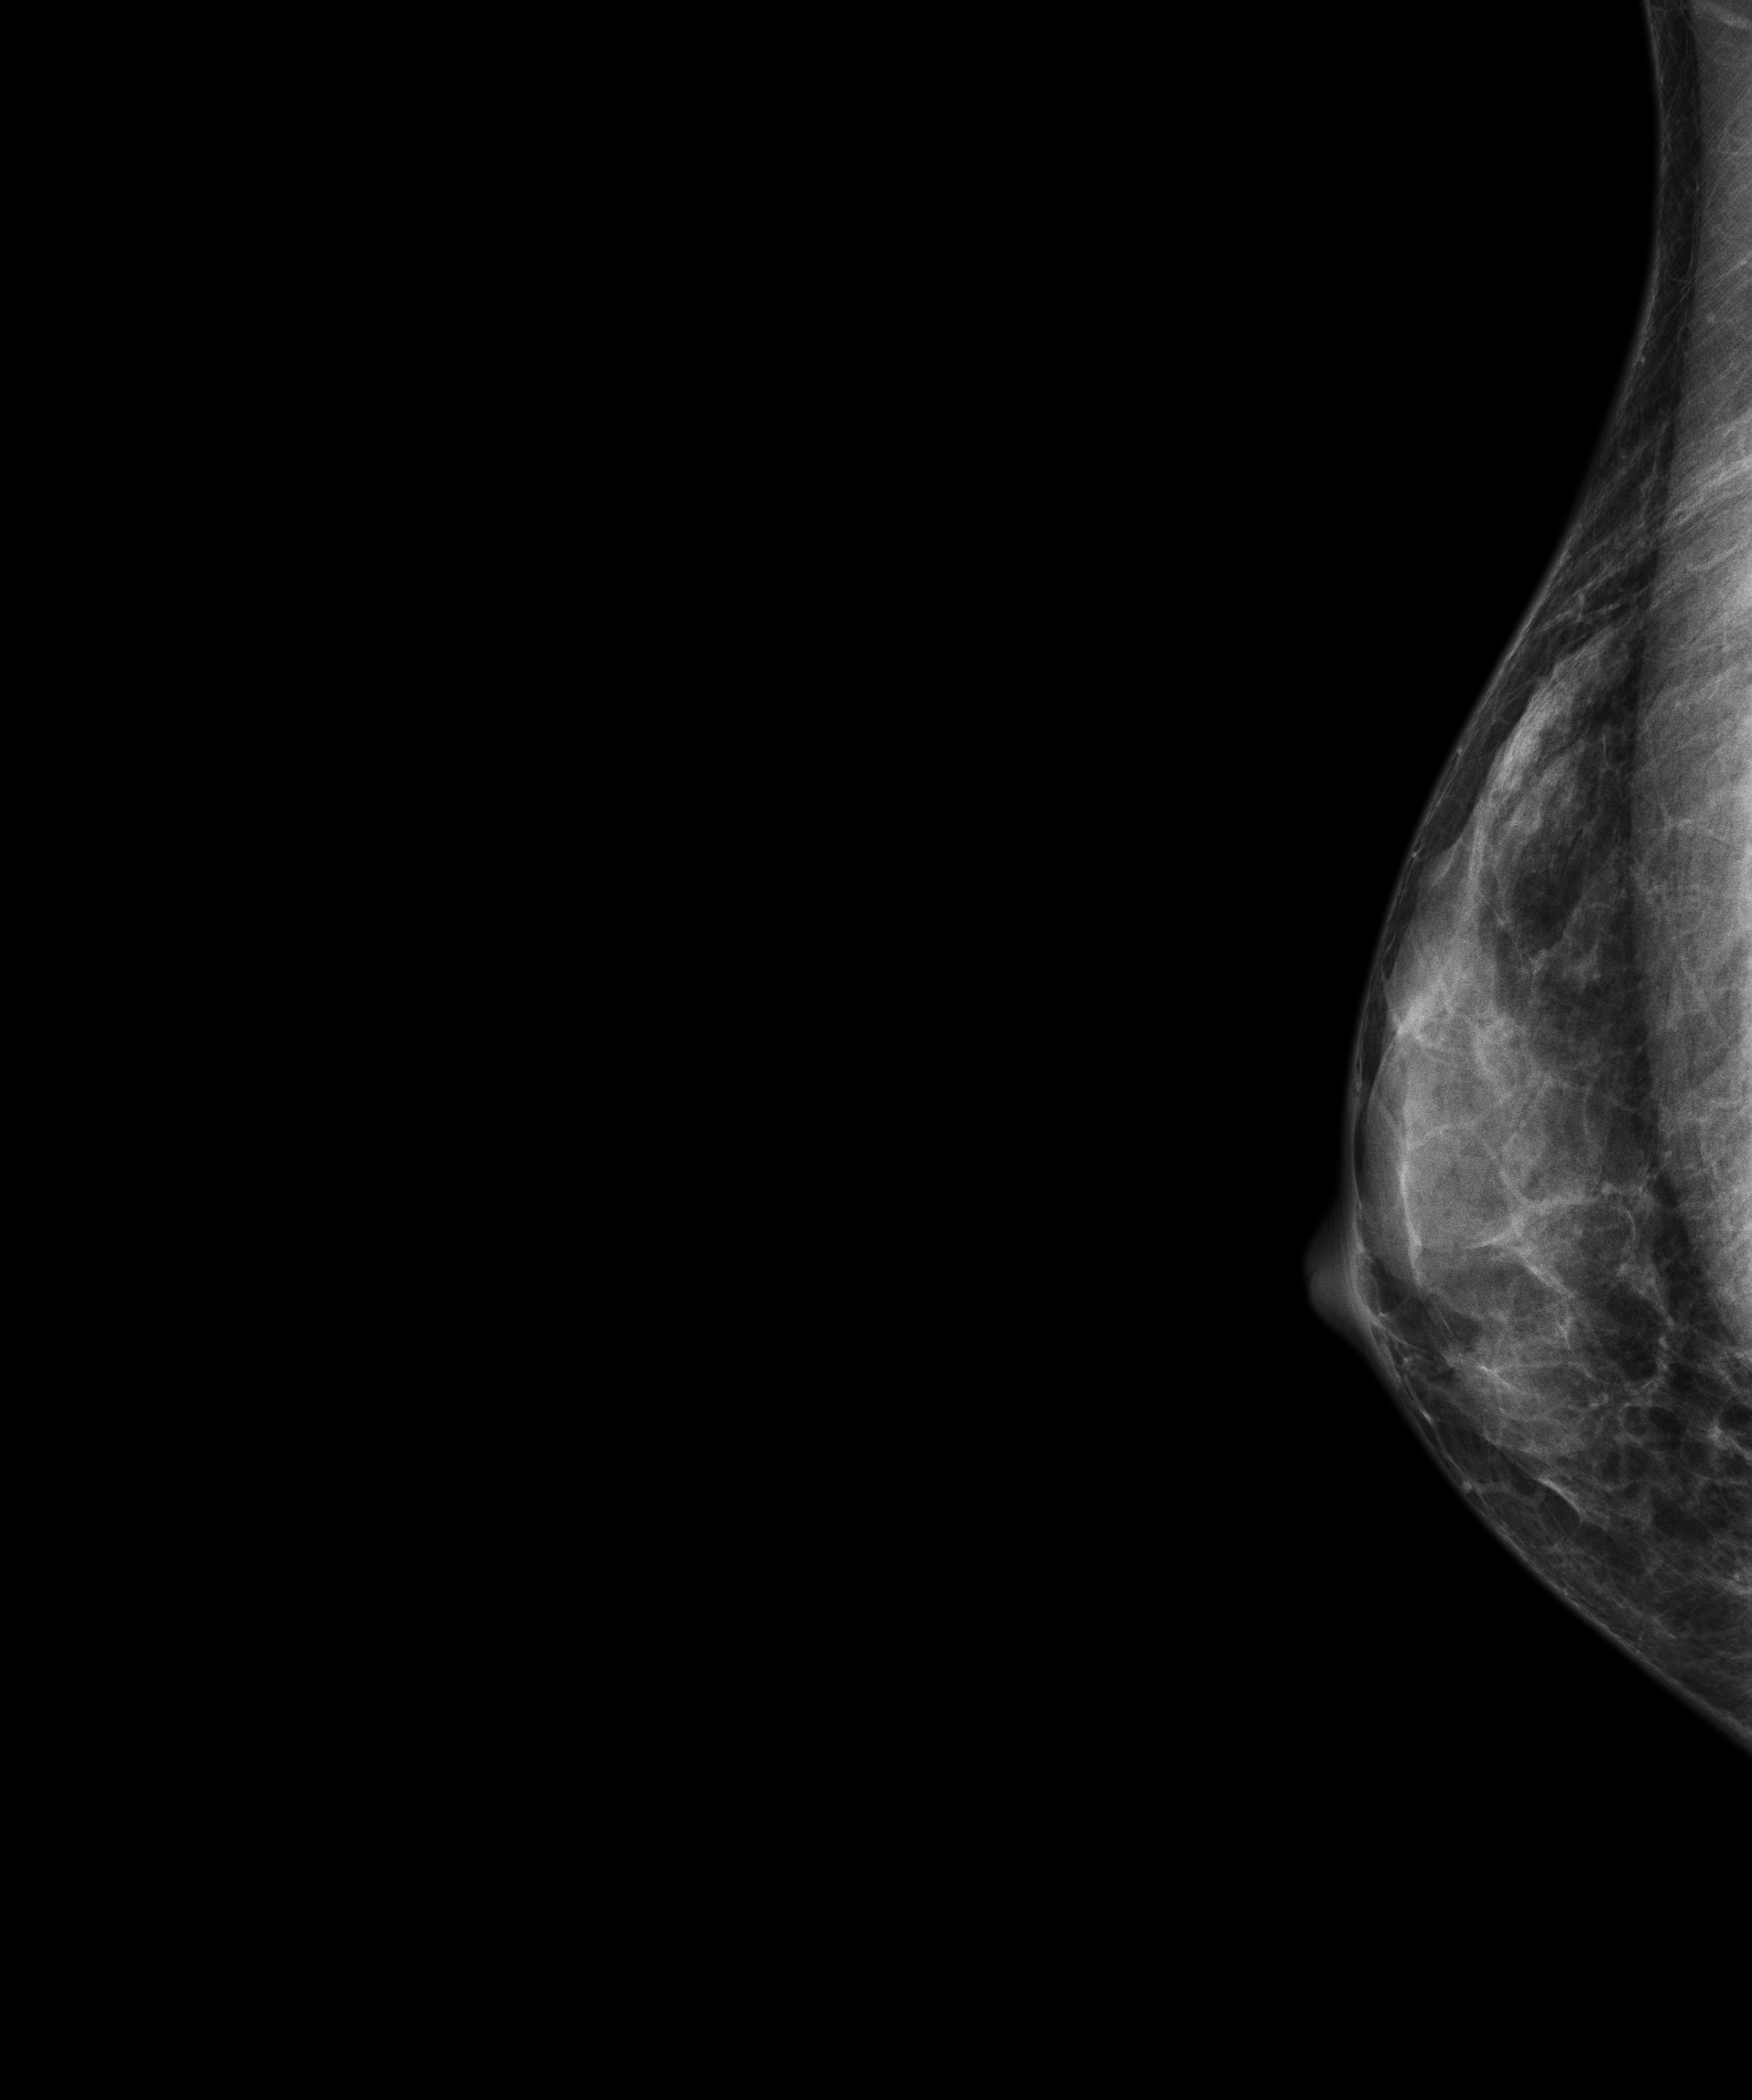
Annual screening mammography examination, compressed breast thickness 31 mm, system: Senographe Essential ADS_56.21.3. Patient aged 55 years (female).
Image type: full-field digital mammogram. Breast: right. Projection: laterally exaggerated craniocaudal (XCCL) view. Breast density at the screening exam (both breasts): extremely dense (BI-RADS density category d). Final BI-RADS category for the screening round (tomosynthesis exam, both breasts): category 1. Recall: no recall after this screen.